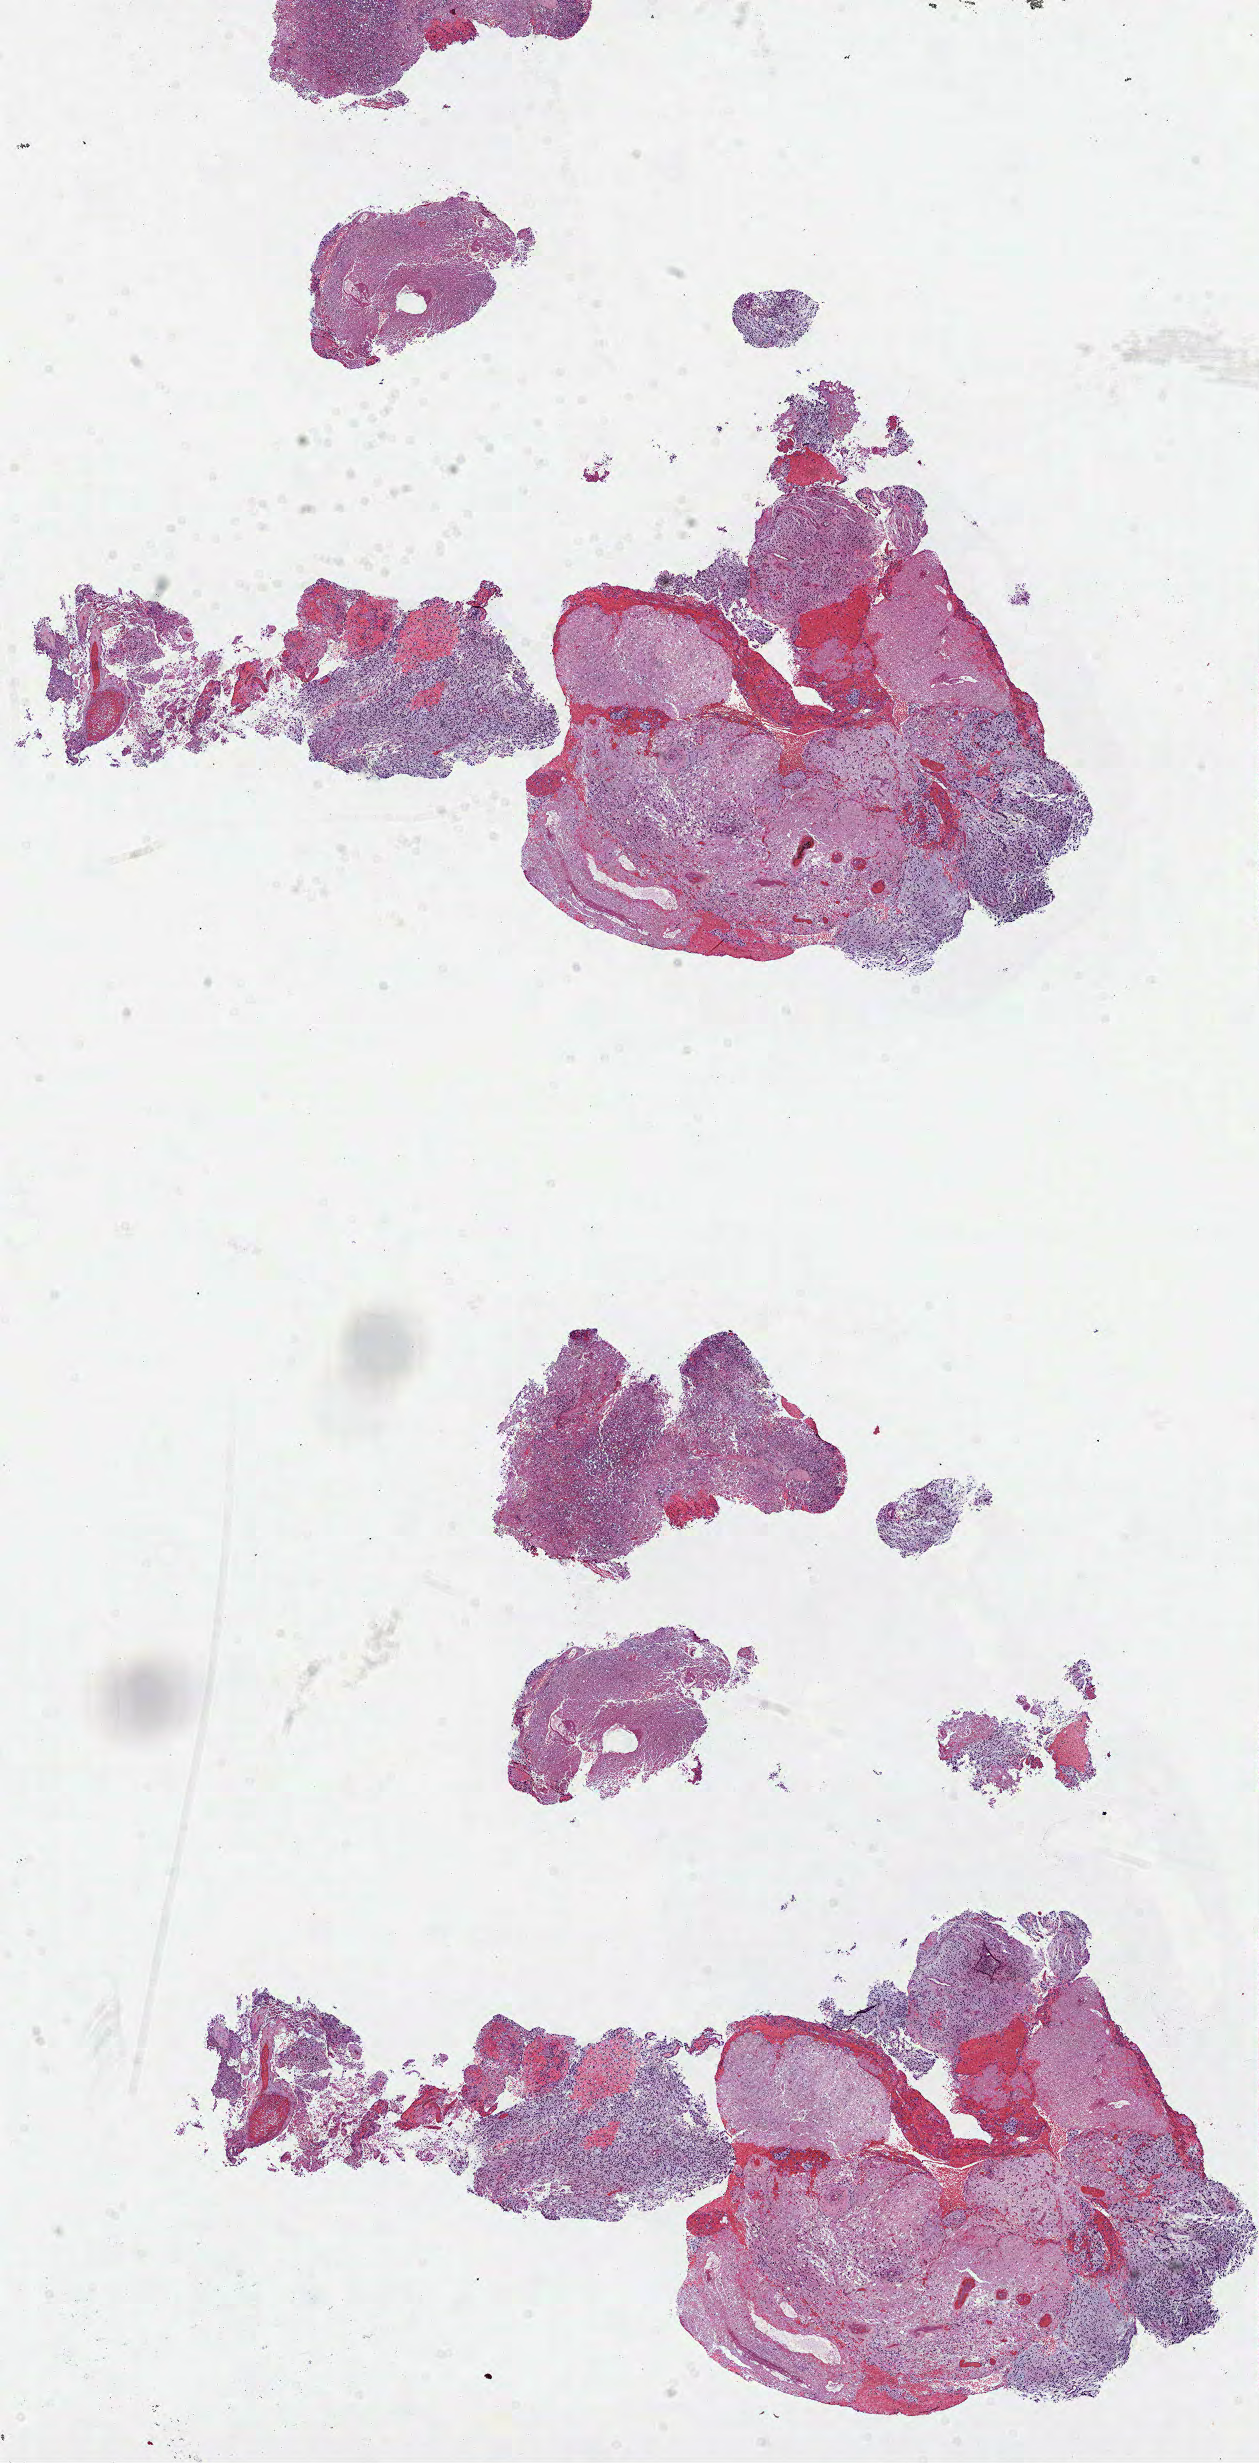
Whole-slide histology image, H&E-stained, whole scanned area (about 10.2 x 19.9 mm, slide scanned at 40x) shown as a low-resolution overview; FFPE section; sample: primary tumour, brain. Female patient; age at initial diagnosis 81 years.
Histologic diagnosis: Glioblastoma.